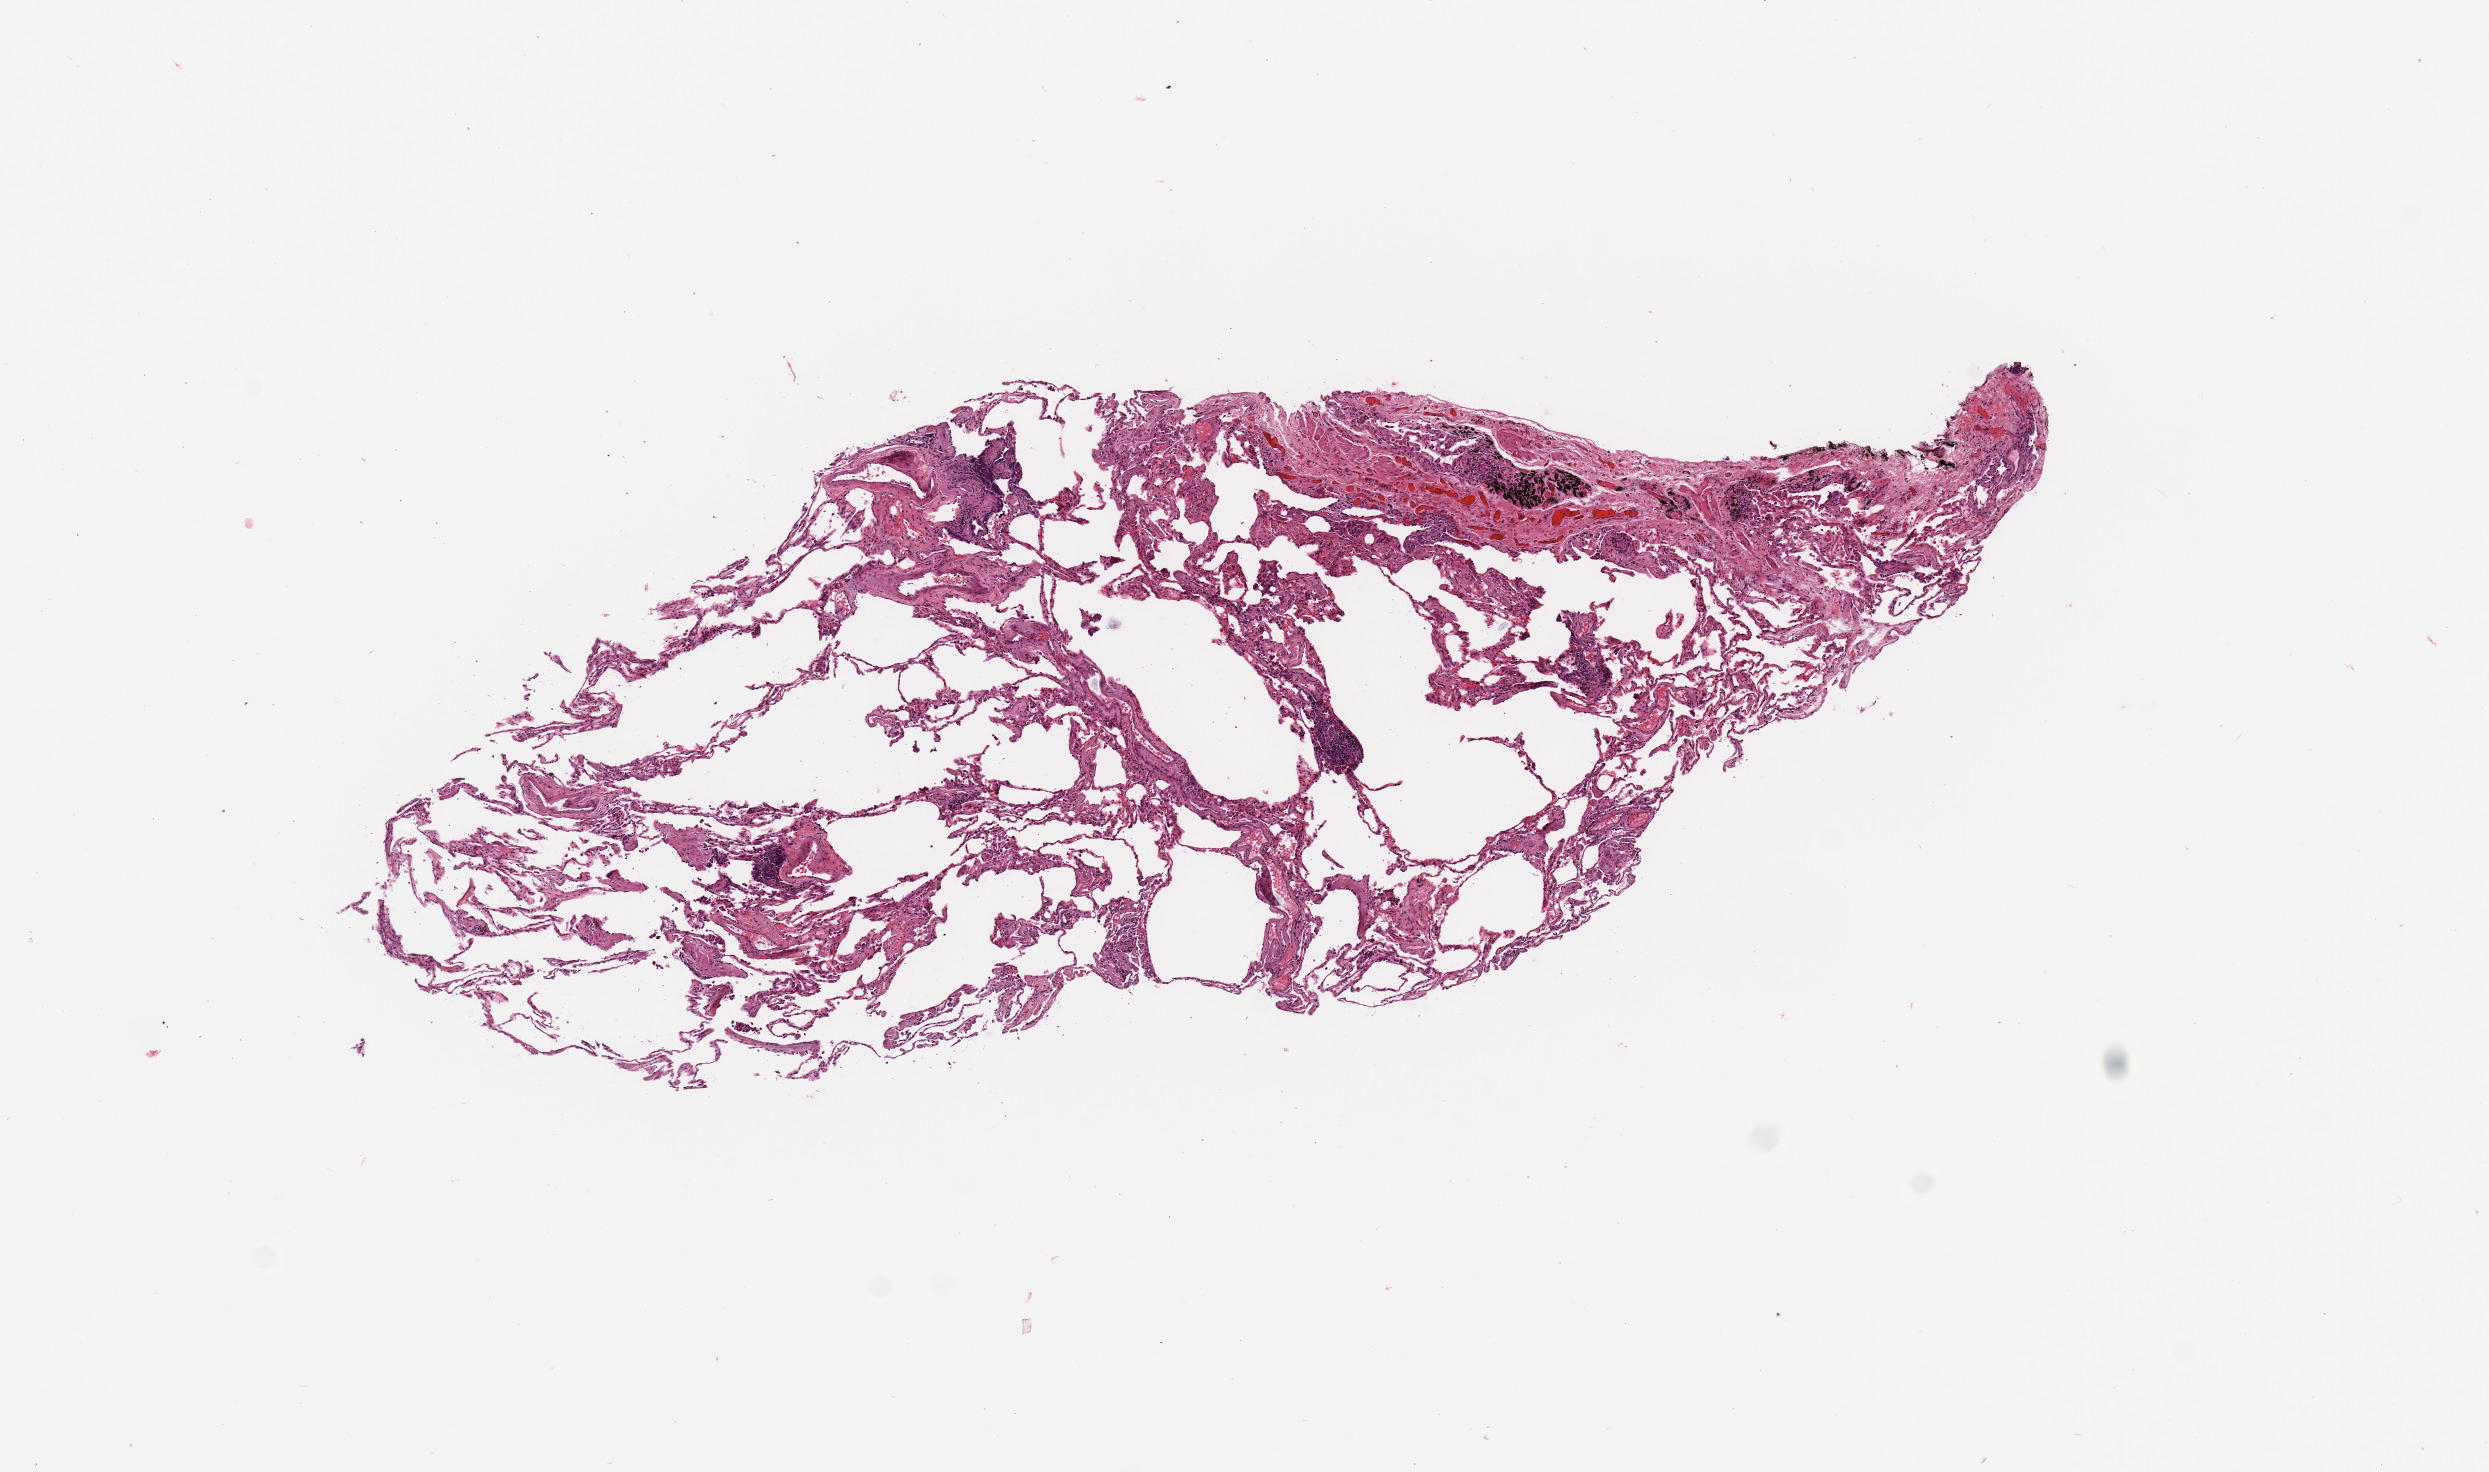
Digitized H&E tissue section (whole slide) — a low-resolution overview of the entire scanned area, about 9.8 x 5.8 mm (slide scanned at 20x), normal (non-tumour) tissue sample, sampled site: lung. Female, 67 y/o.
- this section: normal (non-tumour) tissue from the same patient
- patient diagnosis: Adenocarcinoma, NOS